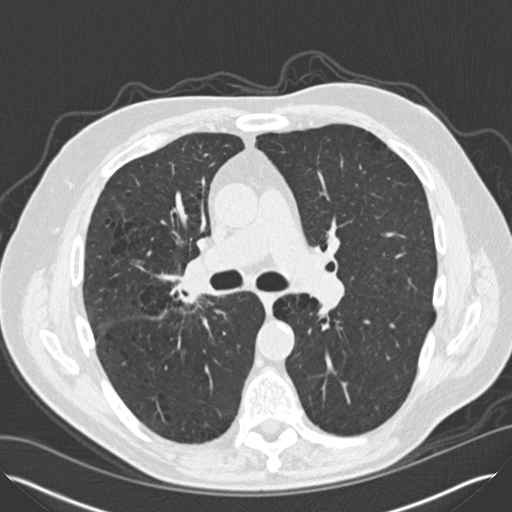
Low-dose screening chest CT, one axial slice. Slice 85 of 149 in the series (ordered by position). Reconstruction kernel B30f. Lung window (W 1500 / L -600 HU). 2 mm slice thickness. 512 × 512 image matrix, field of view 370 × 370 mm.
Outlined on this slice (expert manual segmentation):
- lesion 2 (tumor, hilum of right lung): bounding box (x1, y1, x2, y2) in pixels: (184, 258, 209, 297)